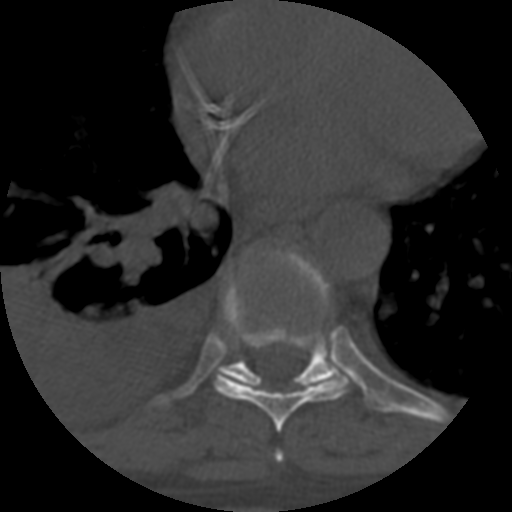
CT including the spine, one axial slice. Position 389 of 708 along the scan axis. Reconstruction kernel STANDARD. 120 kVp. One of 3 acquisitions stored at this slice position. Bone window (W 1800 / L 400 HU). 512 × 512 image matrix. Patient age 55 years. From the clinical record (not read from this slice): primary cancer: colon; vertebrae with lytic lesions (as recorded): T12, L1, L5.
Outlined on this slice (semi-automatic segmentation, software-assisted and operator-edited):
- T7 vertebra: box from (x=274, y=451) to (x=284, y=462) px
- T8 vertebra: (x=213, y=274)–(x=350, y=432)
- T9 vertebra: (x=216, y=249)–(x=340, y=390)